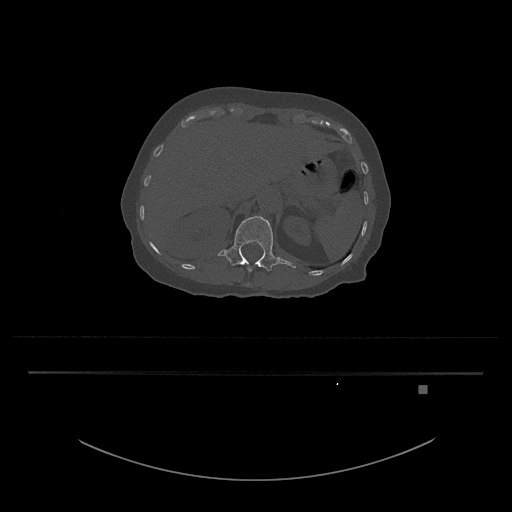
CT including the spine, one axial slice; slice 559 of 797 in the series (ordered by position); 120 kVp; bone window (W 1800 / L 400 HU); 0.5 mm slice thickness; 512 × 512 image matrix. Patient: female, 57 years. Case-level facts recorded for this patient, not image findings: primary cancer: cervical.
Outlined on this slice (semi-automatic segmentation, software-assisted and operator-edited):
- L1 vertebra: bounding box <217,216,296,272> (left, top, right, bottom; pixels)